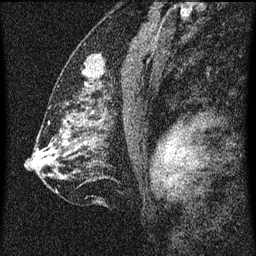
Breast MRI (dynamic contrast-enhanced), one sagittal slice. Slice 40 of 60 in the series (ordered by position). Dynamic contrast-enhanced series, image 2 of 3 at this slice position (ordered by acquisition). 1.5 T. TE 4.2 ms, TR 8 ms. 2 mm slice thickness. 256 × 256 image matrix. Female patient, age 52 years.
Annotated regions visible in this slice (semi-automatically segmented with operator editing):
- analysis volume of interest (the breast-tissue region the enhancement analysis was run in; not a lesion): box from (x=73, y=50) to (x=116, y=101) px
- tumour enhancement mask (voxels above the 70 % enhancement threshold inside the analysis volume of interest): (x=84, y=58)–(x=91, y=75)